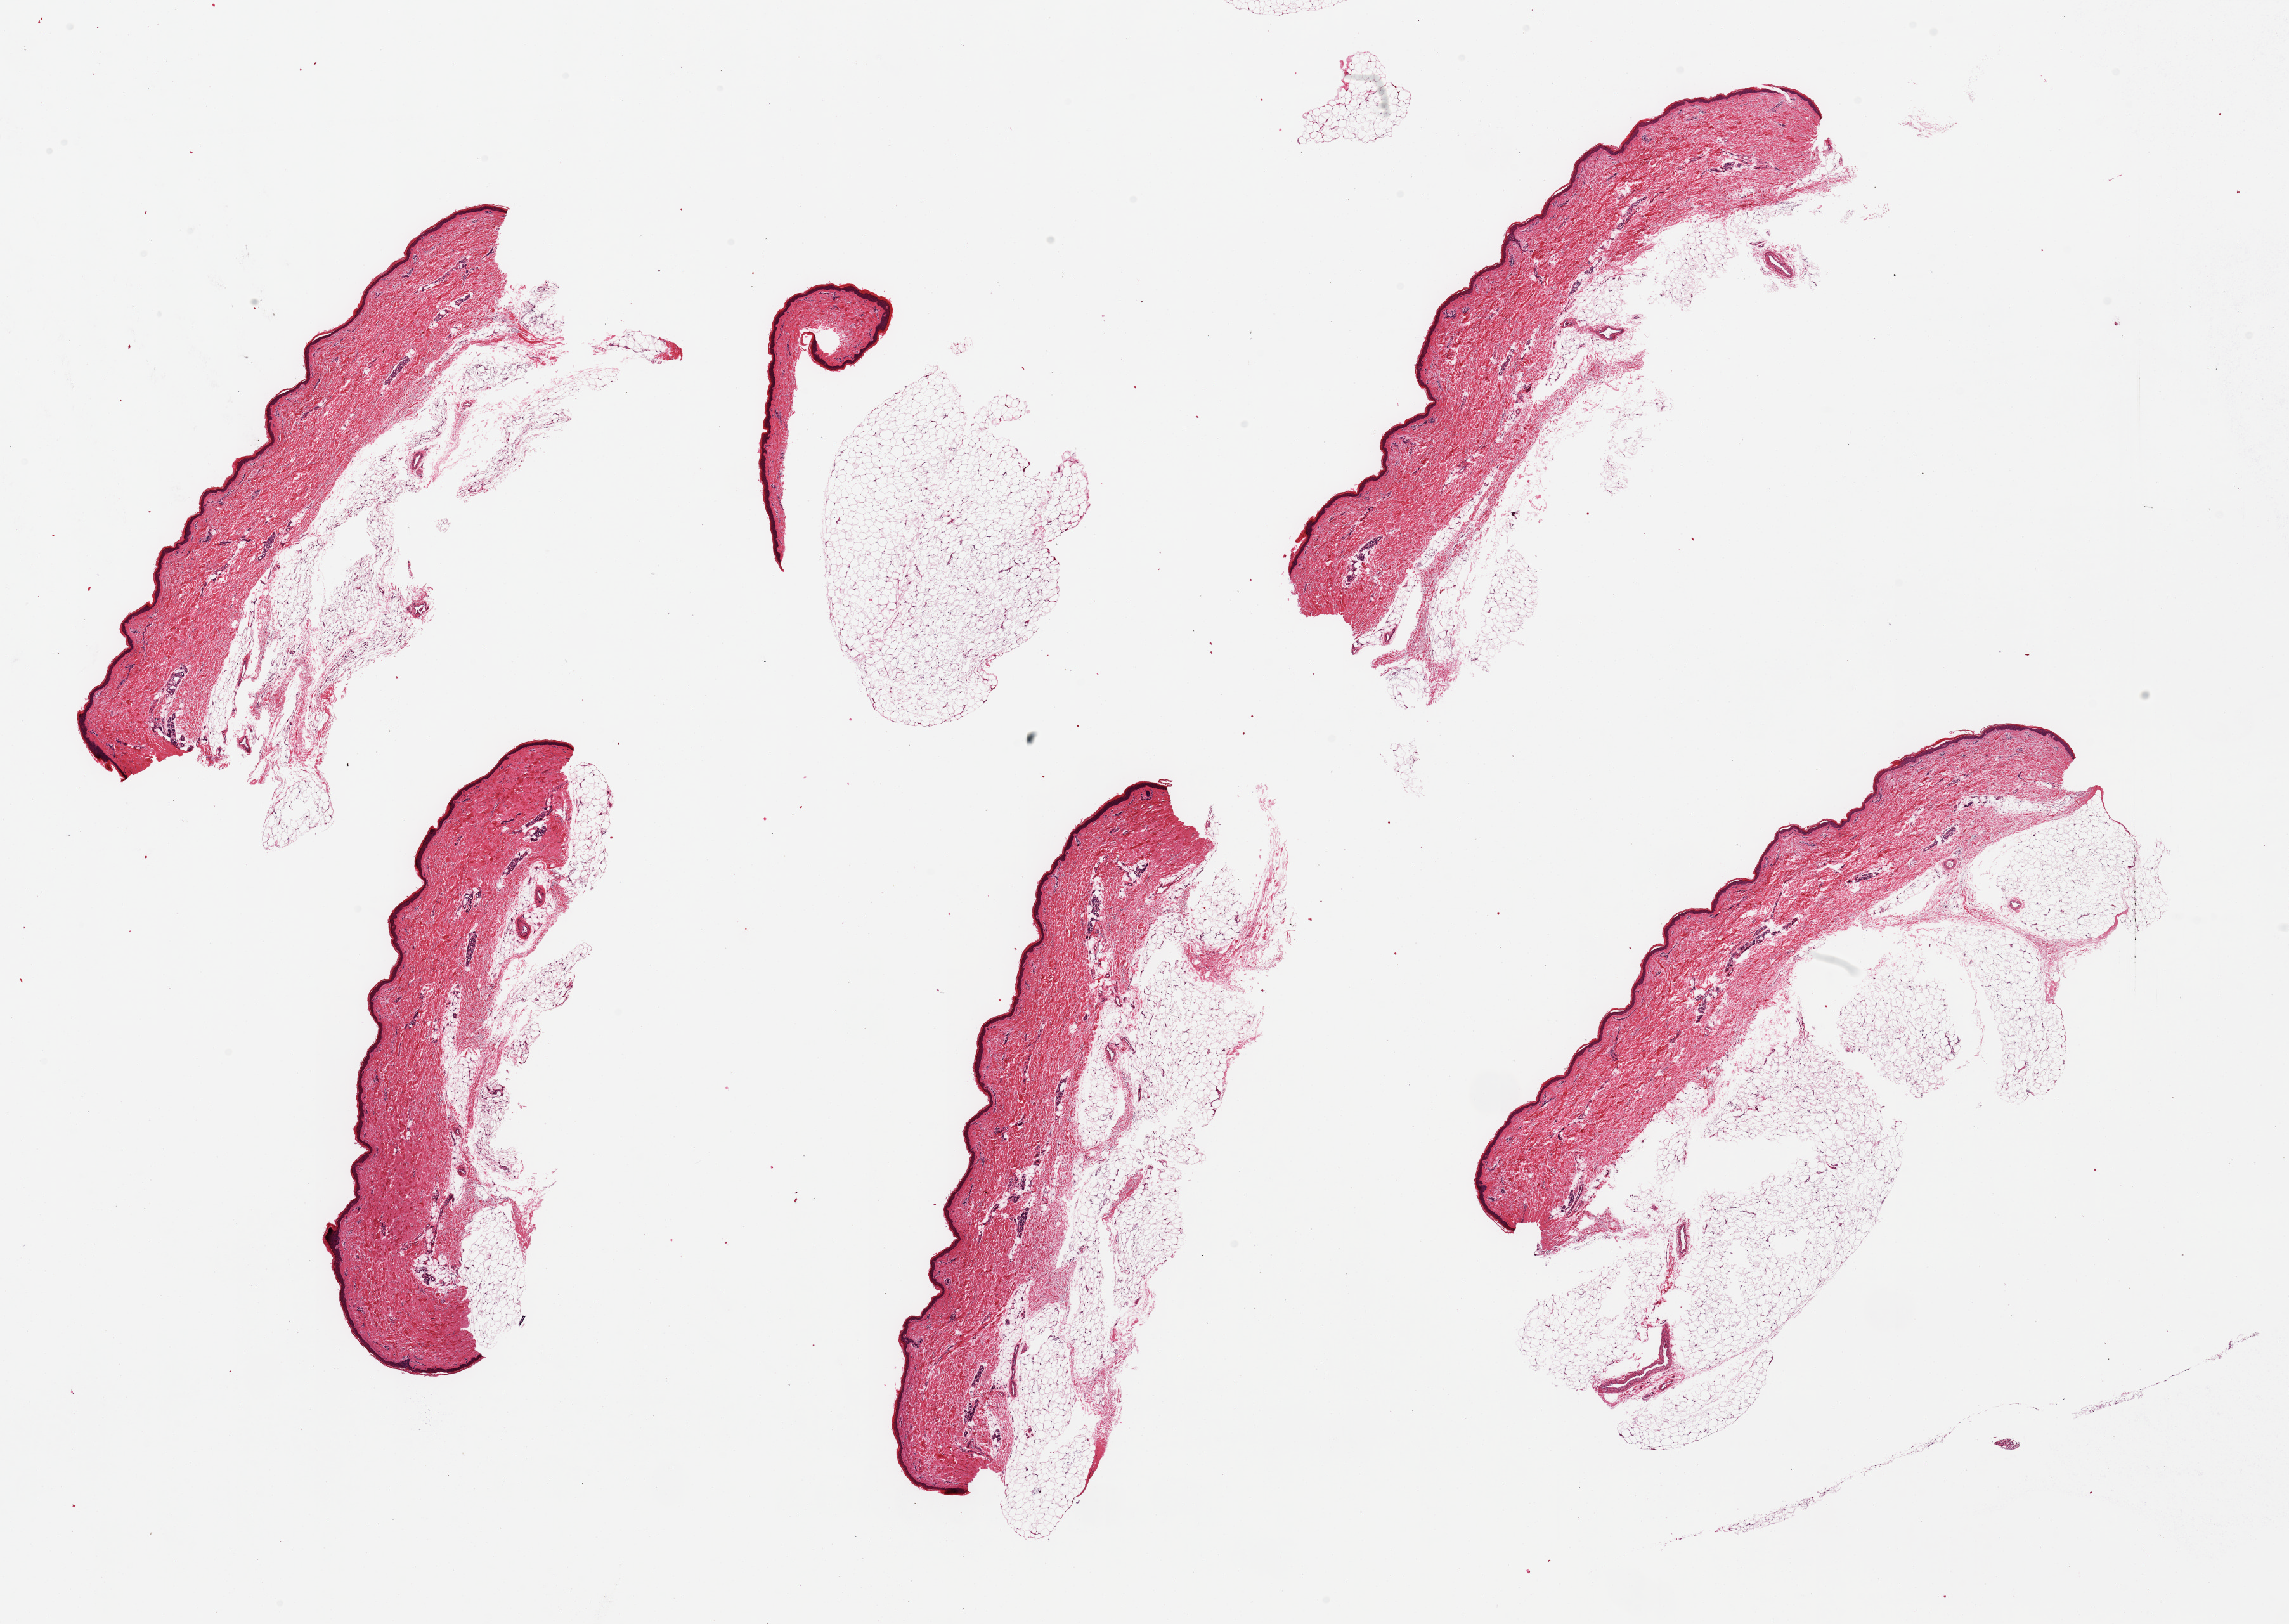
Haematoxylin and eosin whole-slide image — whole scanned area (about 28.5 x 20.3 mm, slide scanned at 20x) shown as a low-resolution overview, PAXgene-fixed, paraffin-embedded tissue, sampled site (target tissue): skin of lower leg, tissue donor sample.
Reviewer comment on this tissue sample: 6 pieces; up to 50% external (subcutaneous) fat; 38.53um thick epidermis; 10% intradermal fat.